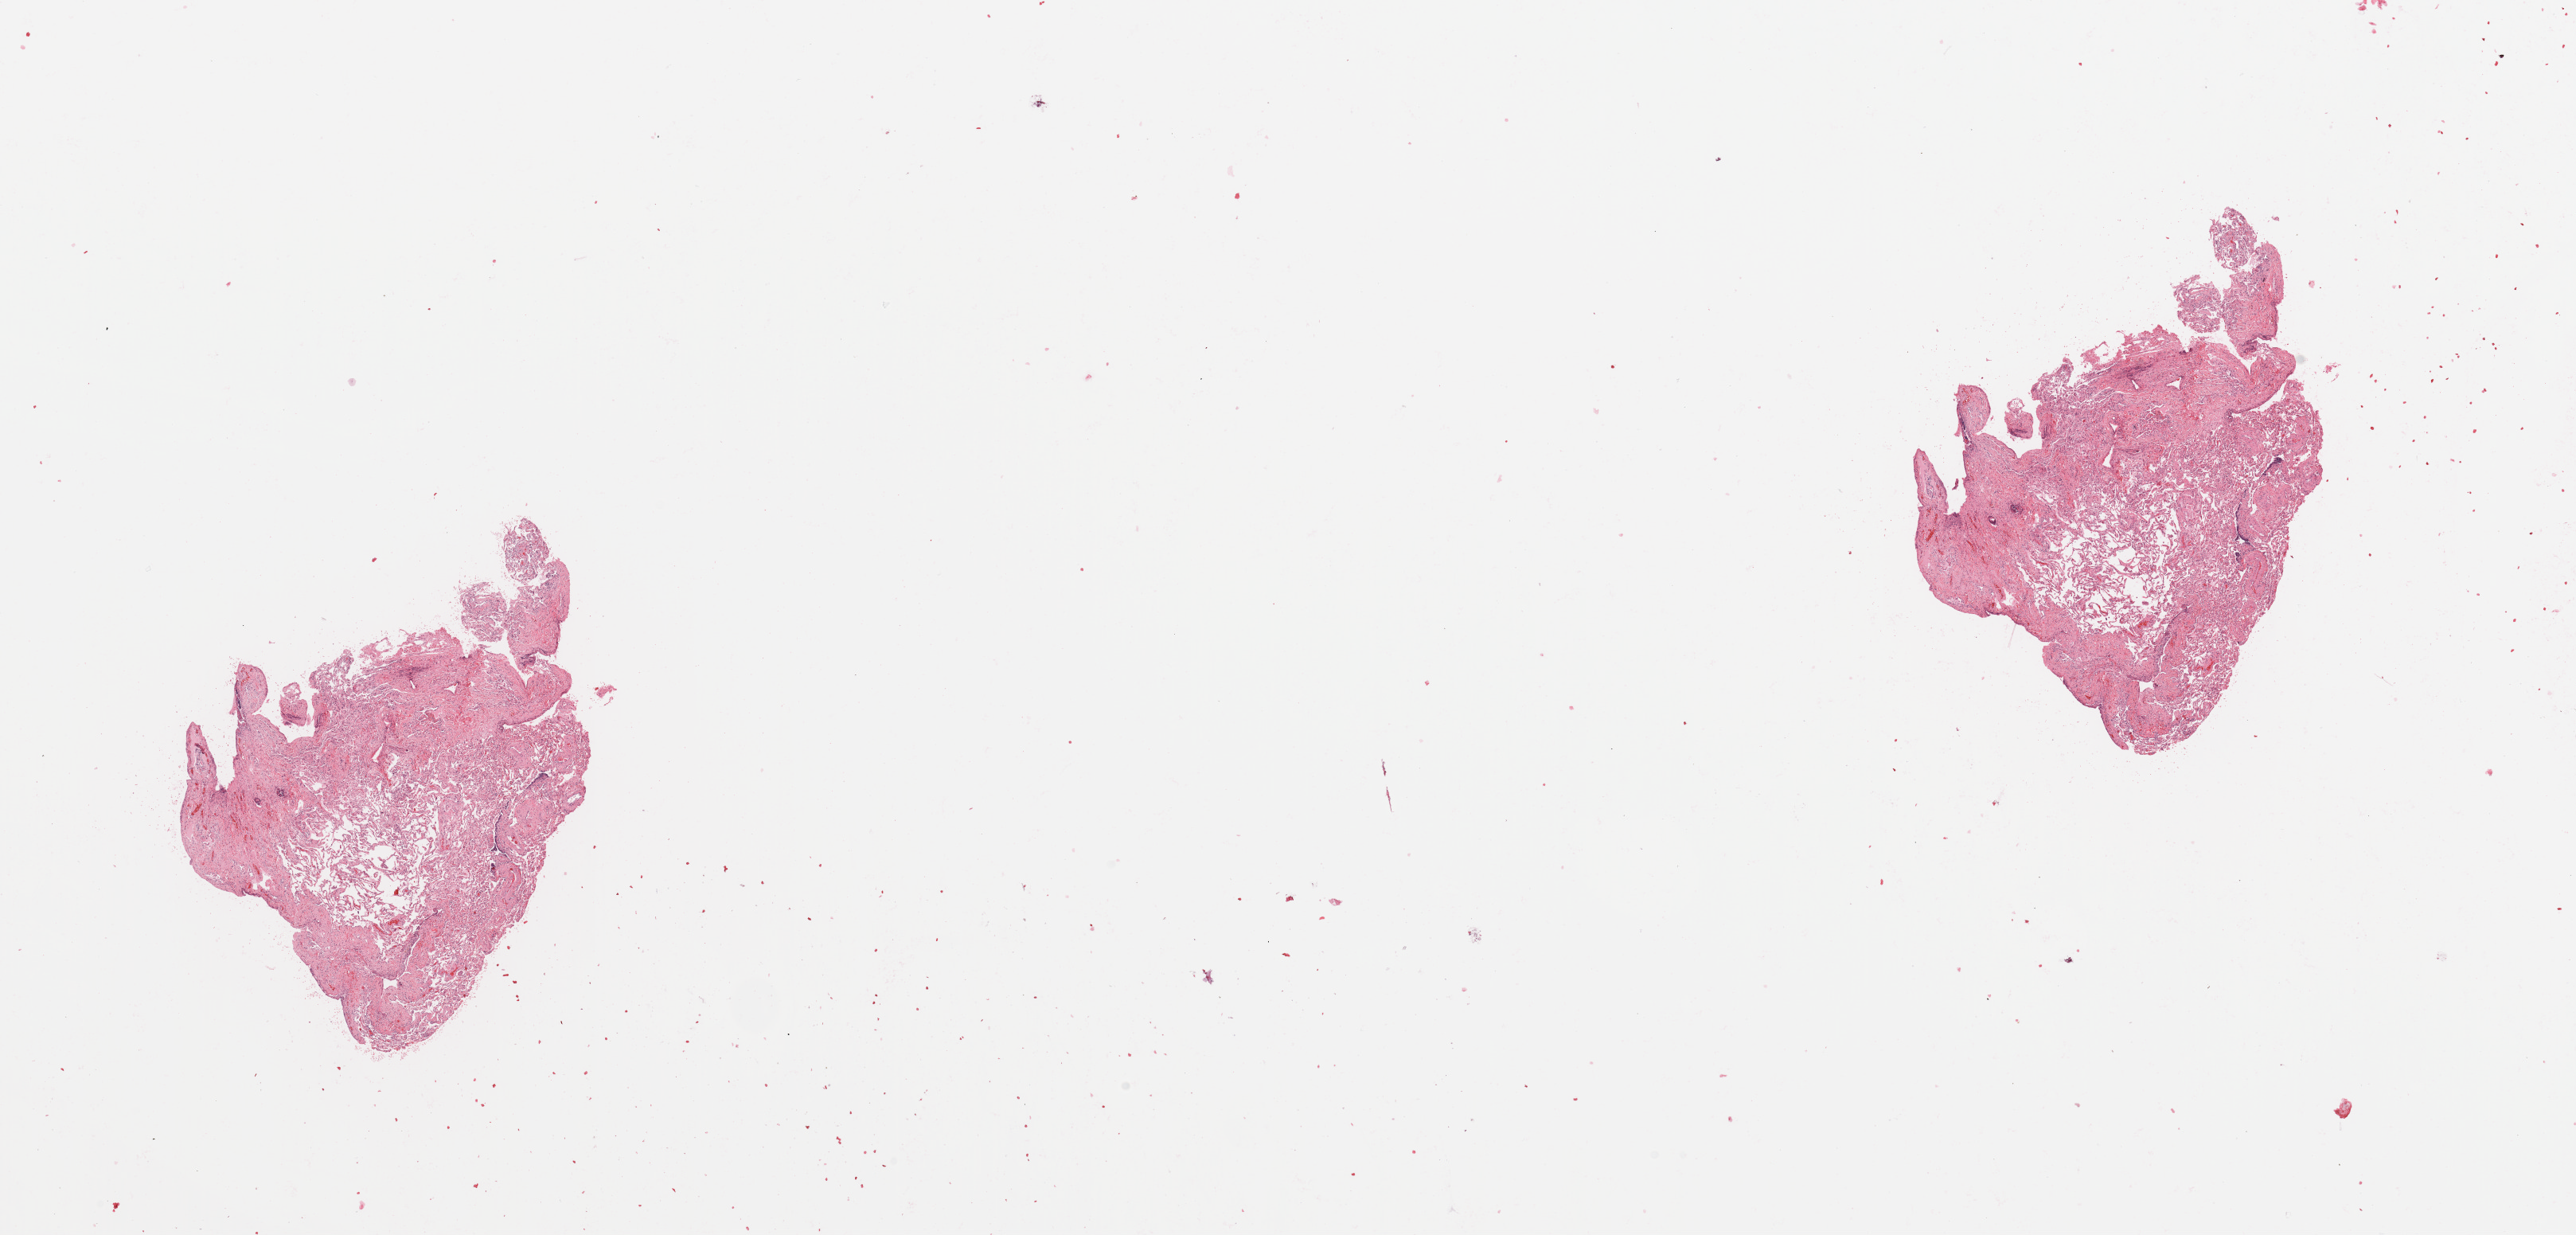
Whole-slide histology image, Hematoxylin and eosin (H&E) stained, low-resolution overview of the scanned area, about 25.6 x 12.3 mm (from a 20x scan), normal (non-tumour) tissue sample, lung. Male, 74 y/o.
* this section: normal (non-tumour) tissue from the same patient
* patient diagnosis: Squamous cell carcinoma, NOS